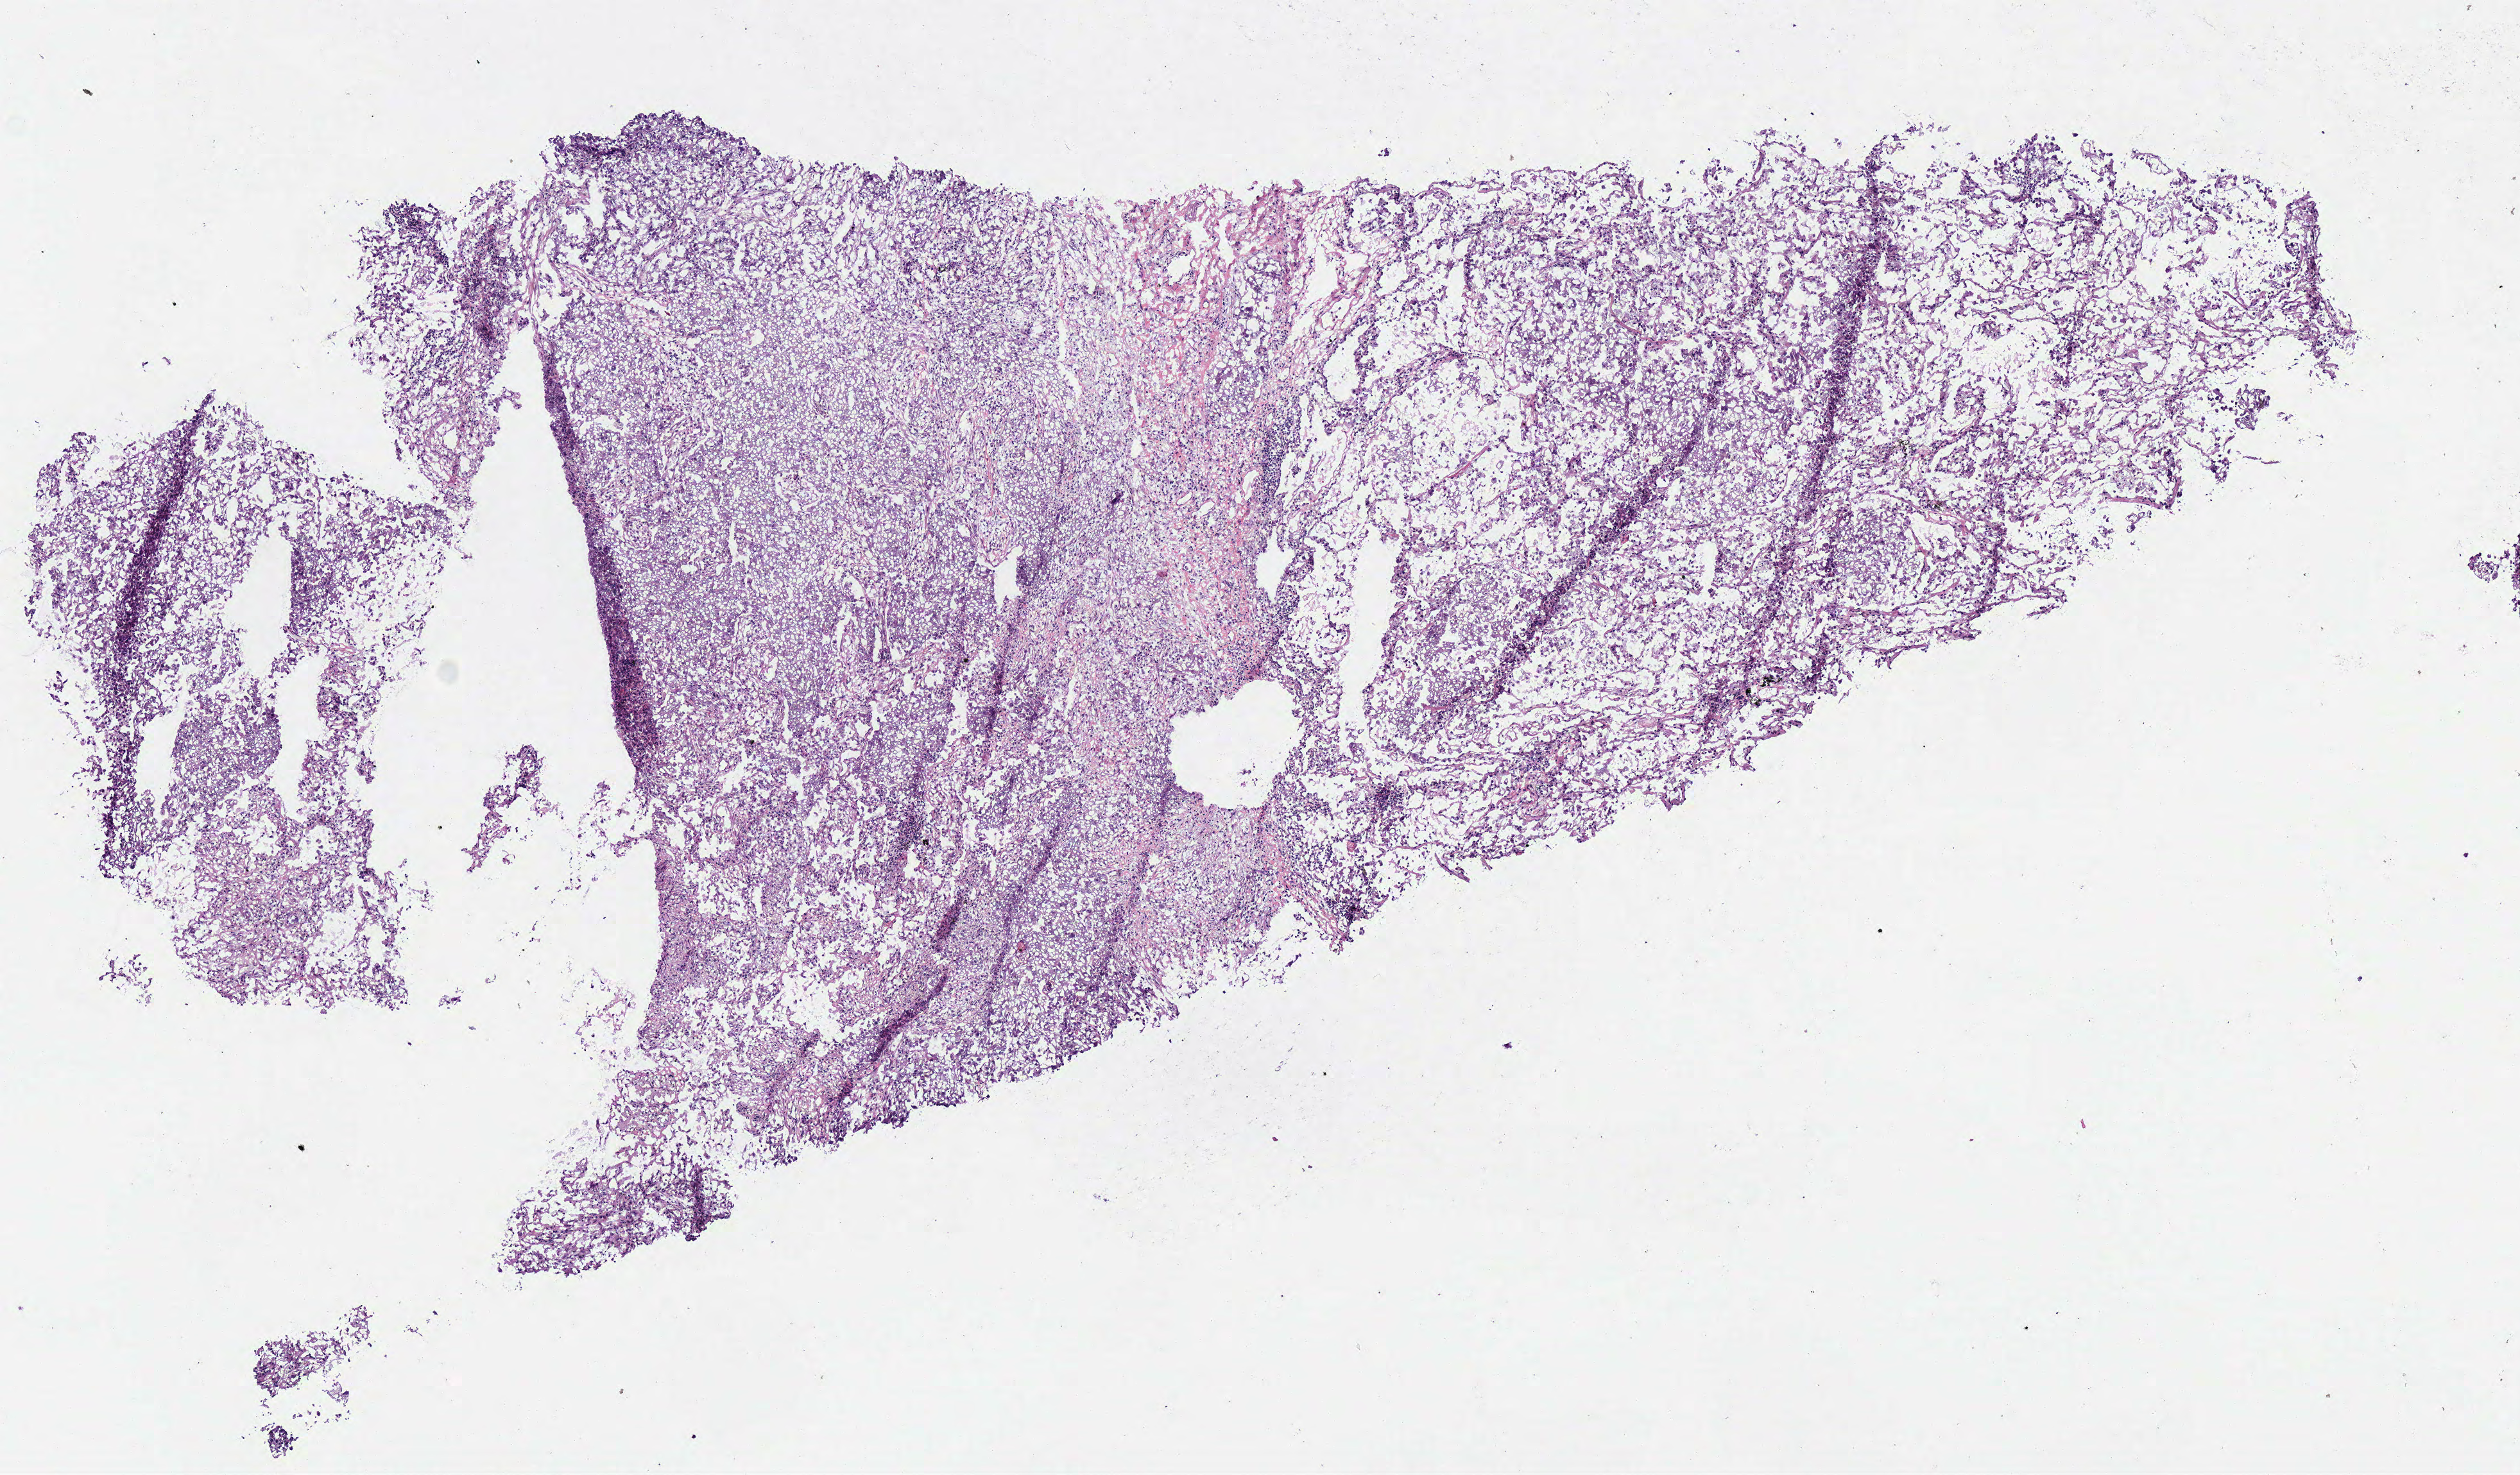
Whole-slide histology image, H&E-stained, shown as a low-resolution overview of the whole scanned area (about 7.7 x 4.5 mm, from a 40x scan); frozen section; sample: primary tumour, lung. Male, age 82 years at initial diagnosis. Pathologist review of this section (percent, as recorded): tumour cells 65%, tumour nuclei 70%, normal cells 20%, stromal cells 15%, necrosis 0%.
* AJCC pathologic stage: IIIA (7th edition)
* histologic diagnosis: Papillary adenocarcinoma, NOS (upper lobe, lung)